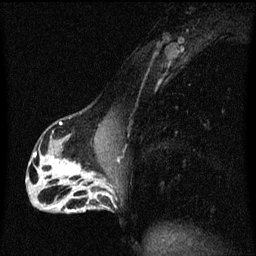
Breast MRI (dynamic contrast-enhanced), one sagittal slice; slice 28 of 60 in the series (ordered by position); dynamic contrast-enhanced series, image 2 of 3 at this slice position (ordered by acquisition); 1.5 T; TE 4.2 ms, TR 8.4 ms; 2 mm slice thickness; 256 × 256 image matrix, field of view 200 × 200 mm. Female patient, age 40 years.
Annotated regions visible in this slice (semi-automatically segmented with operator editing):
- analysis volume of interest (the breast-tissue region the enhancement analysis was run in; not a lesion): bounding box <76,172,114,213> (left, top, right, bottom; pixels)
- tumour enhancement mask (voxels above the 70 % enhancement threshold inside the analysis volume of interest): <76,172,113,211>